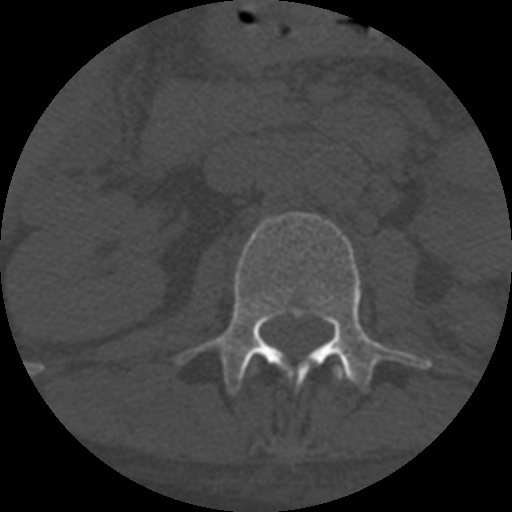
CT including the spine, one axial slice; slice 266 of 708 in the series (ordered by position); reconstruction kernel STANDARD; 120 kVp; one of 3 acquisitions stored at this slice position; bone window (W 1800 / L 400 HU); 512 × 512 image matrix. Patient age 55 years. Case-level facts recorded for this patient, not image findings: primary cancer: colon.
Annotated regions visible in this slice (semi-automatically segmented with operator editing):
- L1 vertebra: bounding box [x1, y1, x2, y2] px = [253, 366, 347, 381]
- L2 vertebra: [174, 212, 431, 395]